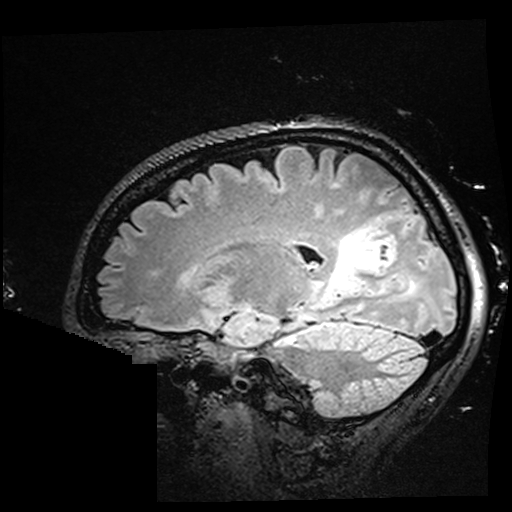
Brain MRI from a brain-tumour surgery series, one sagittal slice; slice 110 of 176 in the series (ordered by position); T2 FLAIR; 1 mm slice thickness; 512 × 512 image matrix, field of view 250 × 250 mm. From the clinical record (not read from this slice): histopathology: Oligodendroglioma; WHO grade: 2; IDH mutation: yes; tumour location: Right Parietal.
Annotated regions visible in this slice (manually delineated by an expert):
- residual tumour: bounding box (x1, y1, x2, y2) in pixels: (325, 229, 386, 294)